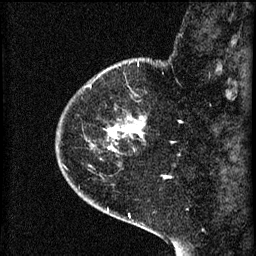
Breast MRI (dynamic contrast-enhanced), one sagittal slice; slice 14 of 60 in the series (ordered by position); 3 images stored at this slice position (order not interpretable as contrast timing); 1.5 T; TE 4.2 ms, TR 8.2 ms; 256 × 256 image matrix, field of view 180 × 180 mm. Female patient, age 44 years.
Annotated regions visible in this slice (semi-automatic segmentation, software-assisted and operator-edited):
- analysis volume of interest (the breast-tissue region the enhancement analysis was run in; not a lesion): bounding box [x1, y1, x2, y2] px = [73, 82, 147, 165]
- tumour enhancement mask (voxels above the 70 % enhancement threshold inside the analysis volume of interest): [90, 86, 145, 151]